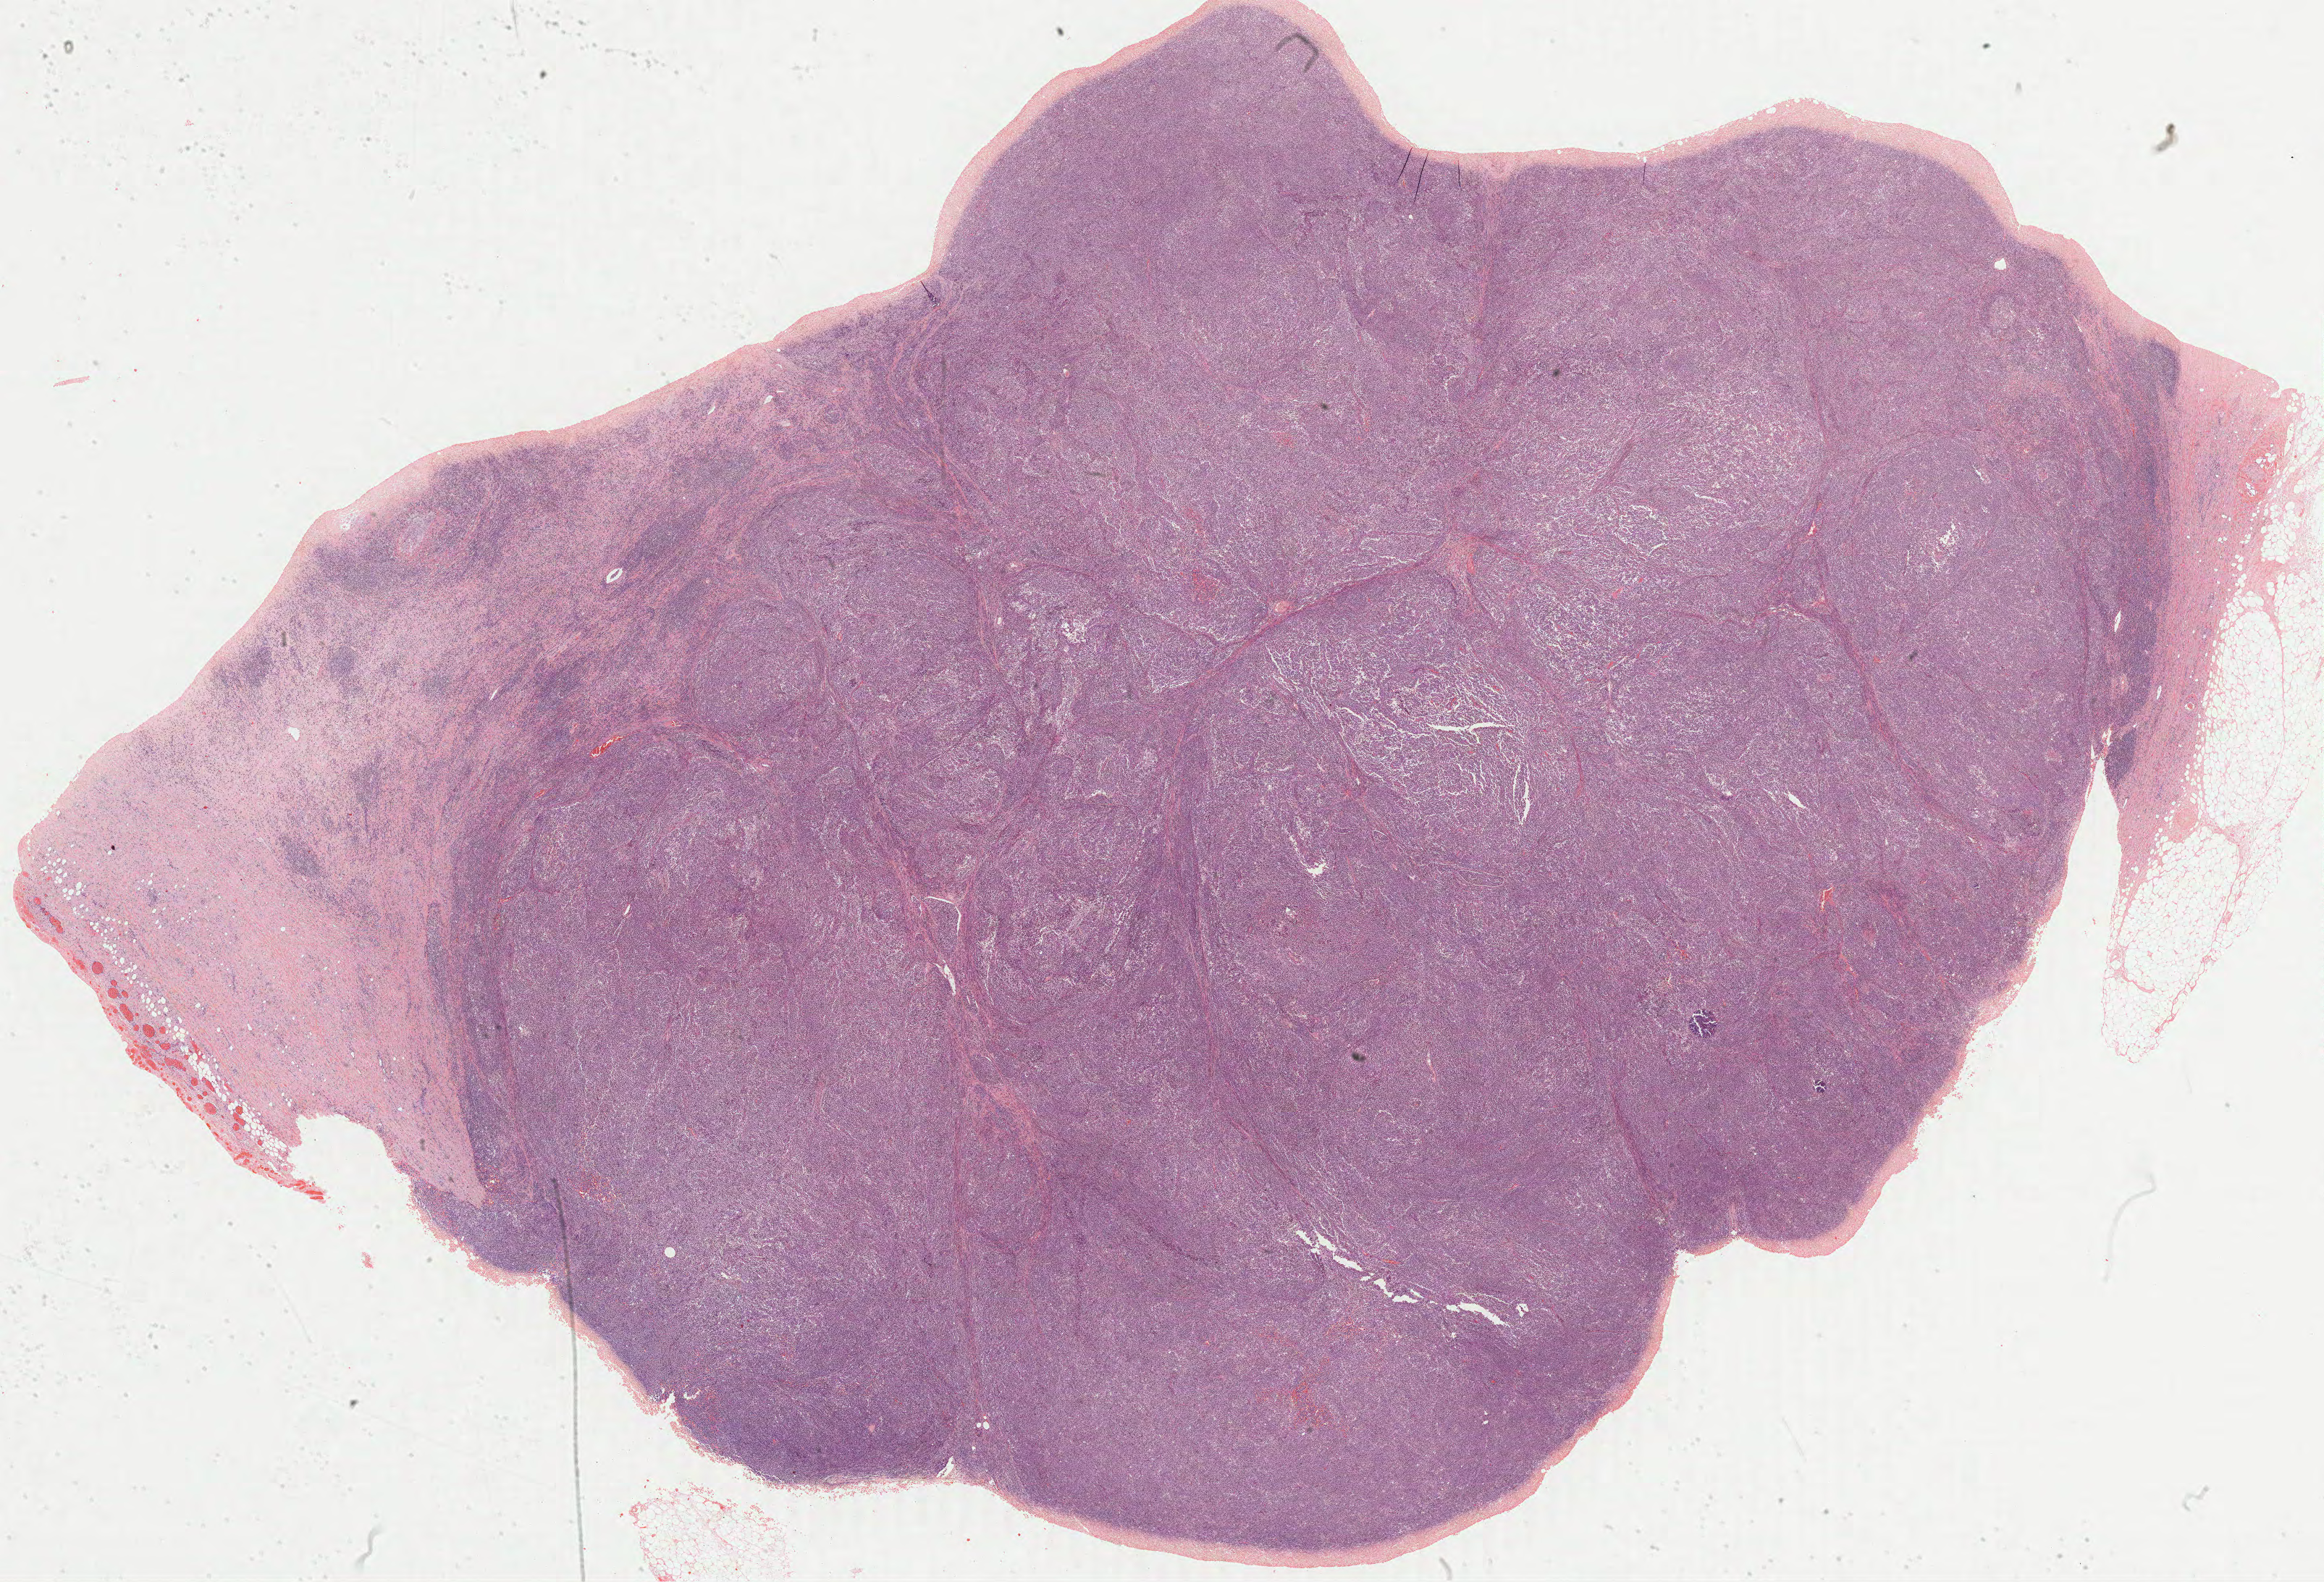
Whole-slide histology image, H&E — a low-resolution overview of the entire scanned area, about 25.7 x 17.5 mm (slide scanned at 40x). Formalin-fixed paraffin-embedded (FFPE) diagnostic section. Metastatic tumour sample. Male patient; age at initial diagnosis 52 years.
This section: metastatic tumour tissue. Patient diagnosis: Malignant melanoma, NOS.